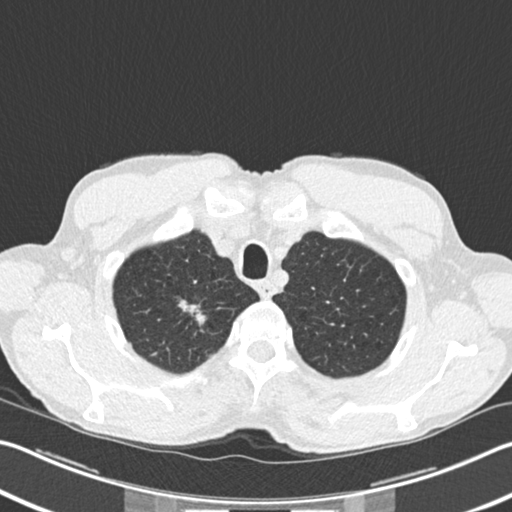
Low-dose screening chest CT, one axial slice; slice 192 of 220 in the series (ordered by position); reconstruction kernel B30f; lung window (W 1500 / L -600 HU); 2 mm slice thickness; 512 × 512 image matrix, field of view 342 × 342 mm.
Outlined on this slice (expert manual segmentation):
- lesion 1 (tumor, upper lobe of right lung): bounding box [x1, y1, x2, y2] px = [179, 300, 205, 324]